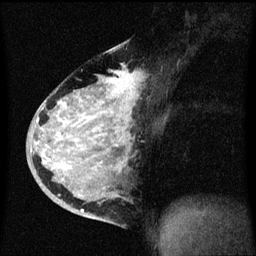
Breast MRI (dynamic contrast-enhanced), one sagittal slice. Slice 36 of 60 in the series (ordered by position). Dynamic contrast-enhanced series, image 2 of 3 at this slice position (ordered by acquisition). 1.5 T. TE 4.2 ms, TR 8.4 ms. 2 mm slice thickness. 256 × 256 image matrix, field of view 200 × 200 mm. Female patient, age 34 years. Case-level facts recorded for this patient, not image findings: setting: breast cancer imaged before/during neoadjuvant chemotherapy; receptor status: HR-positive, HER2-negative.
Annotated regions visible in this slice (semi-automatic segmentation, software-assisted and operator-edited):
- analysis volume of interest (the breast-tissue region the enhancement analysis was run in; not a lesion): bounding box <34,48,135,215> (left, top, right, bottom; pixels)
- tumour enhancement mask (voxels above the 70 % enhancement threshold inside the analysis volume of interest): <36,72,131,213>